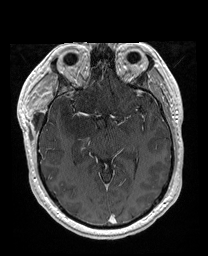
Brain MRI from a brain-tumour surgery series, one axial slice. Position 106 of 176 along the scan axis. T1-weighted post-contrast. 1 mm slice thickness. 208 × 256 image matrix, field of view 208 × 256 mm. Case-level facts recorded for this patient, not image findings: histopathology: Astrocytoma; WHO grade: 4; IDH mutation: yes; tumour location: Right Orbitofrontal Anterior Temporal Insular.
Structures marked on this image (manually delineated by an expert):
- previous resection cavity: box from (x=56, y=60) to (x=106, y=74) px